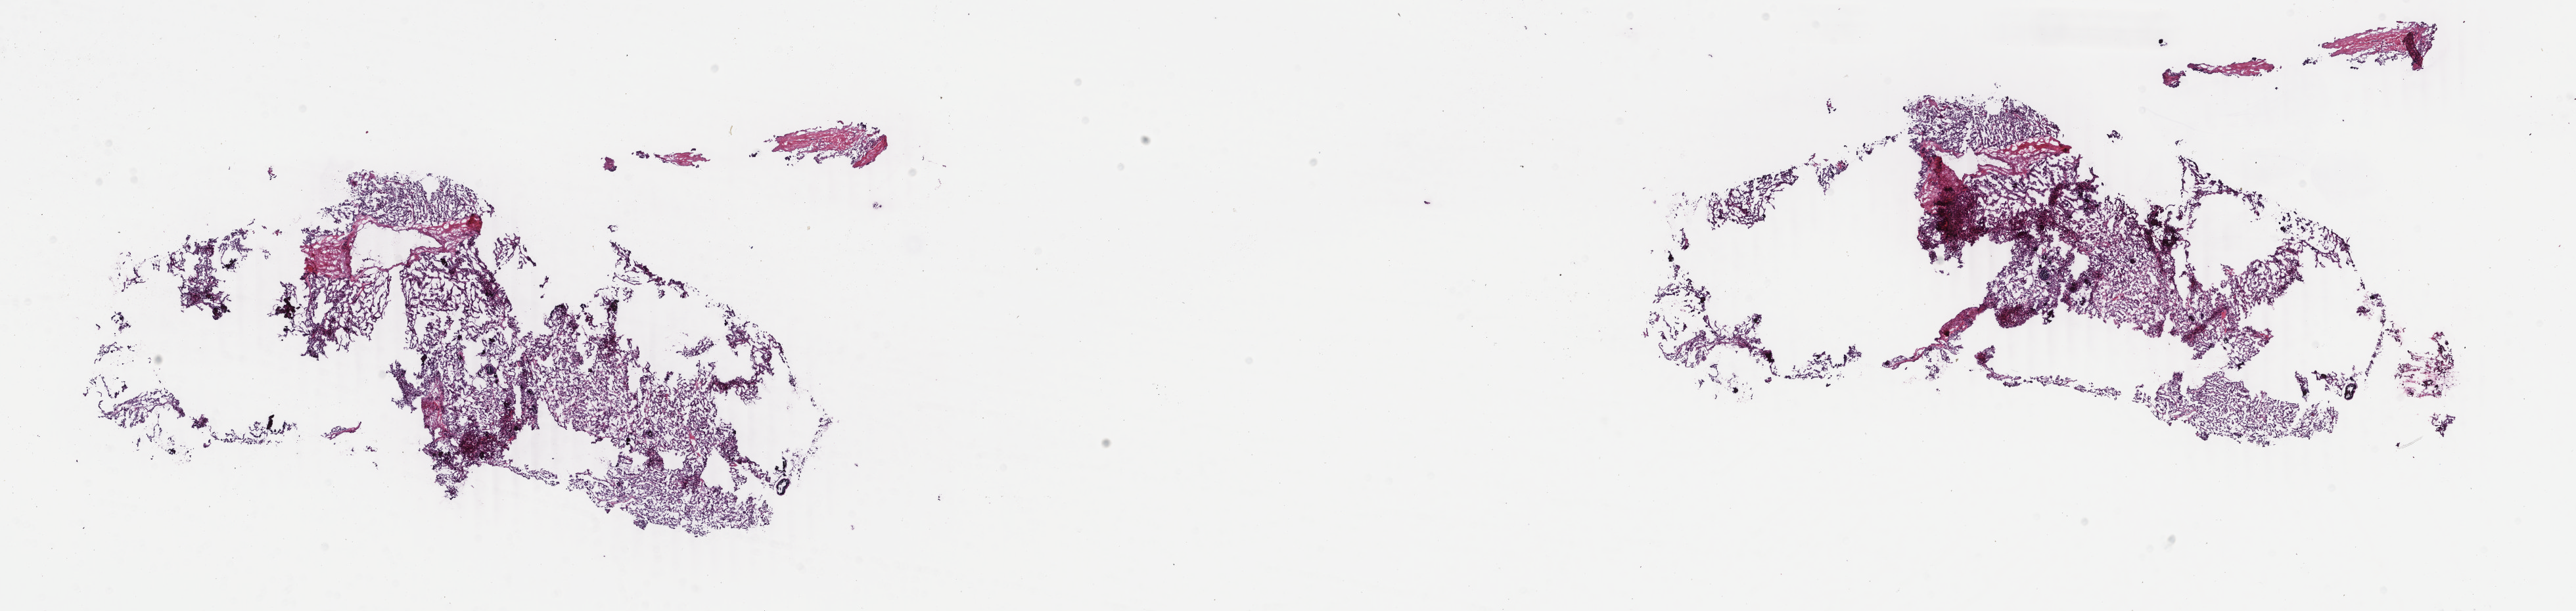
H&E-stained whole-slide image, a low-resolution overview of the entire scanned area, about 31.2 x 7.4 mm. Frozen section from the bottom of the tissue portion. Sample: primary tumour, thyroid. Female, age 30 years at initial diagnosis. Pathologist review of this section (percent, as recorded): tumour cells 80%, tumour nuclei 80%, normal cells 0%, stromal cells 20%, necrosis 0%. Inflammatory infiltration, as recorded: lymphocyte infiltration 2%, monocyte infiltration 0%, neutrophil infiltration 0%.
• laterality: left
• AJCC pathologic stage: I (6th edition)
• lymph nodes positive (case pathology): 2 of 2 examined
• histologic diagnosis: Papillary adenocarcinoma, NOS (thyroid gland)